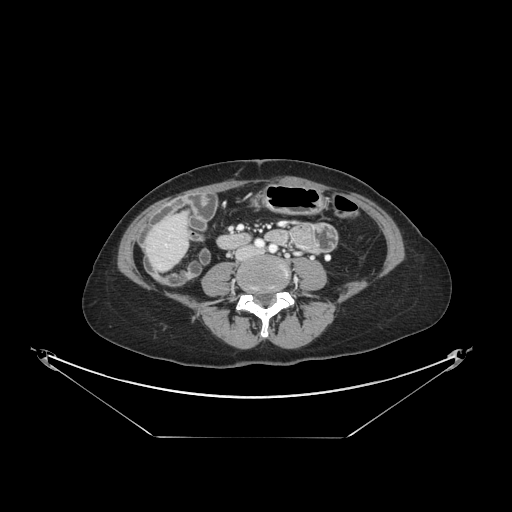
Contrast-enhanced abdominal CT, one axial slice. Position 25 of 148 along the scan axis. Intravenous contrast given. Soft-tissue window (W 400 / L 40 HU). 2.5 mm slice thickness. 512 × 512 image matrix, field of view 500 × 500 mm. Female patient, age 73 years. Case-level facts recorded for this patient, not image findings: diagnosis: colorectal cancer liver metastases, imaged before liver resection; multiple liver metastases: no; largest metastasis: 1 cm; disease in both lobes: no.
Annotated regions visible in this slice (expert manual segmentation):
- liver: box from (x=150, y=216) to (x=186, y=268) px
- planned liver remnant (the part of the liver to remain after resection): (x=168, y=215)–(x=185, y=234)